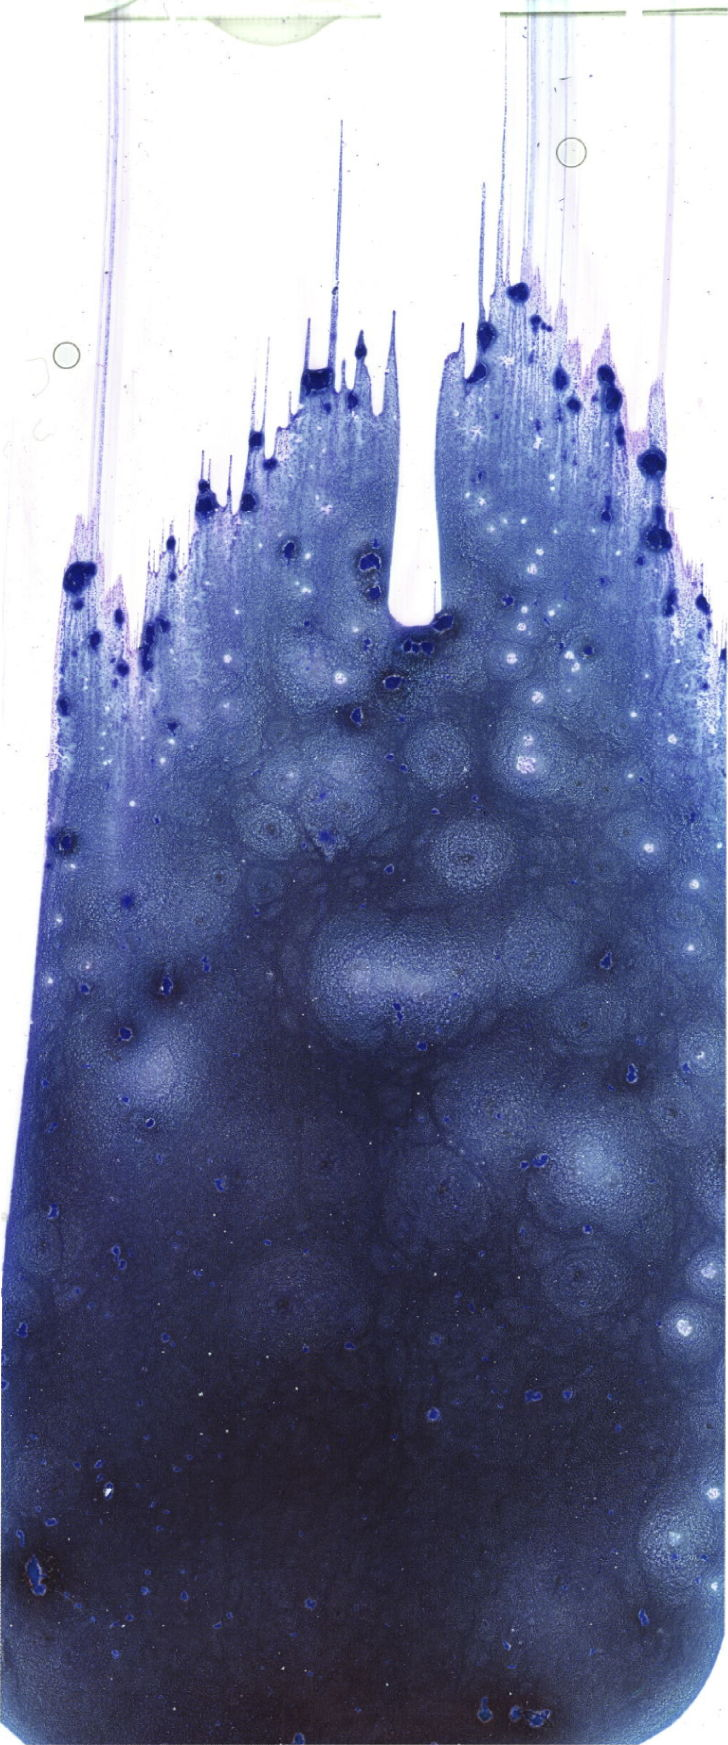
May-Grünwald–Giemsa-stained marrow aspirate smear (whole slide), shown as a low-resolution overview of the whole scanned area (about 20.6 x 49.5 mm). Patient sex: female.
* diagnosis: Acute Myeloid Leukemia with Maturation